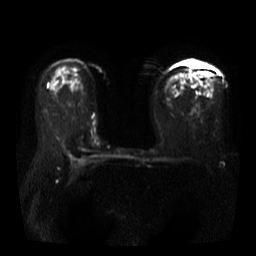
Breast MRI, one axial slice. Position 24 of 40 along the scan axis. Diffusion-weighted series; image 2 of 4 stored at this slice position (different b-values; order by instance number). 3 T. 5 mm slice thickness. 256 × 256 image matrix, field of view 360 × 360 mm. Female patient.
Annotated regions visible in this slice (expert manual segmentation):
- tumour on diffusion-weighted imaging: bounding box (x1, y1, x2, y2) in pixels: (188, 61, 198, 67)